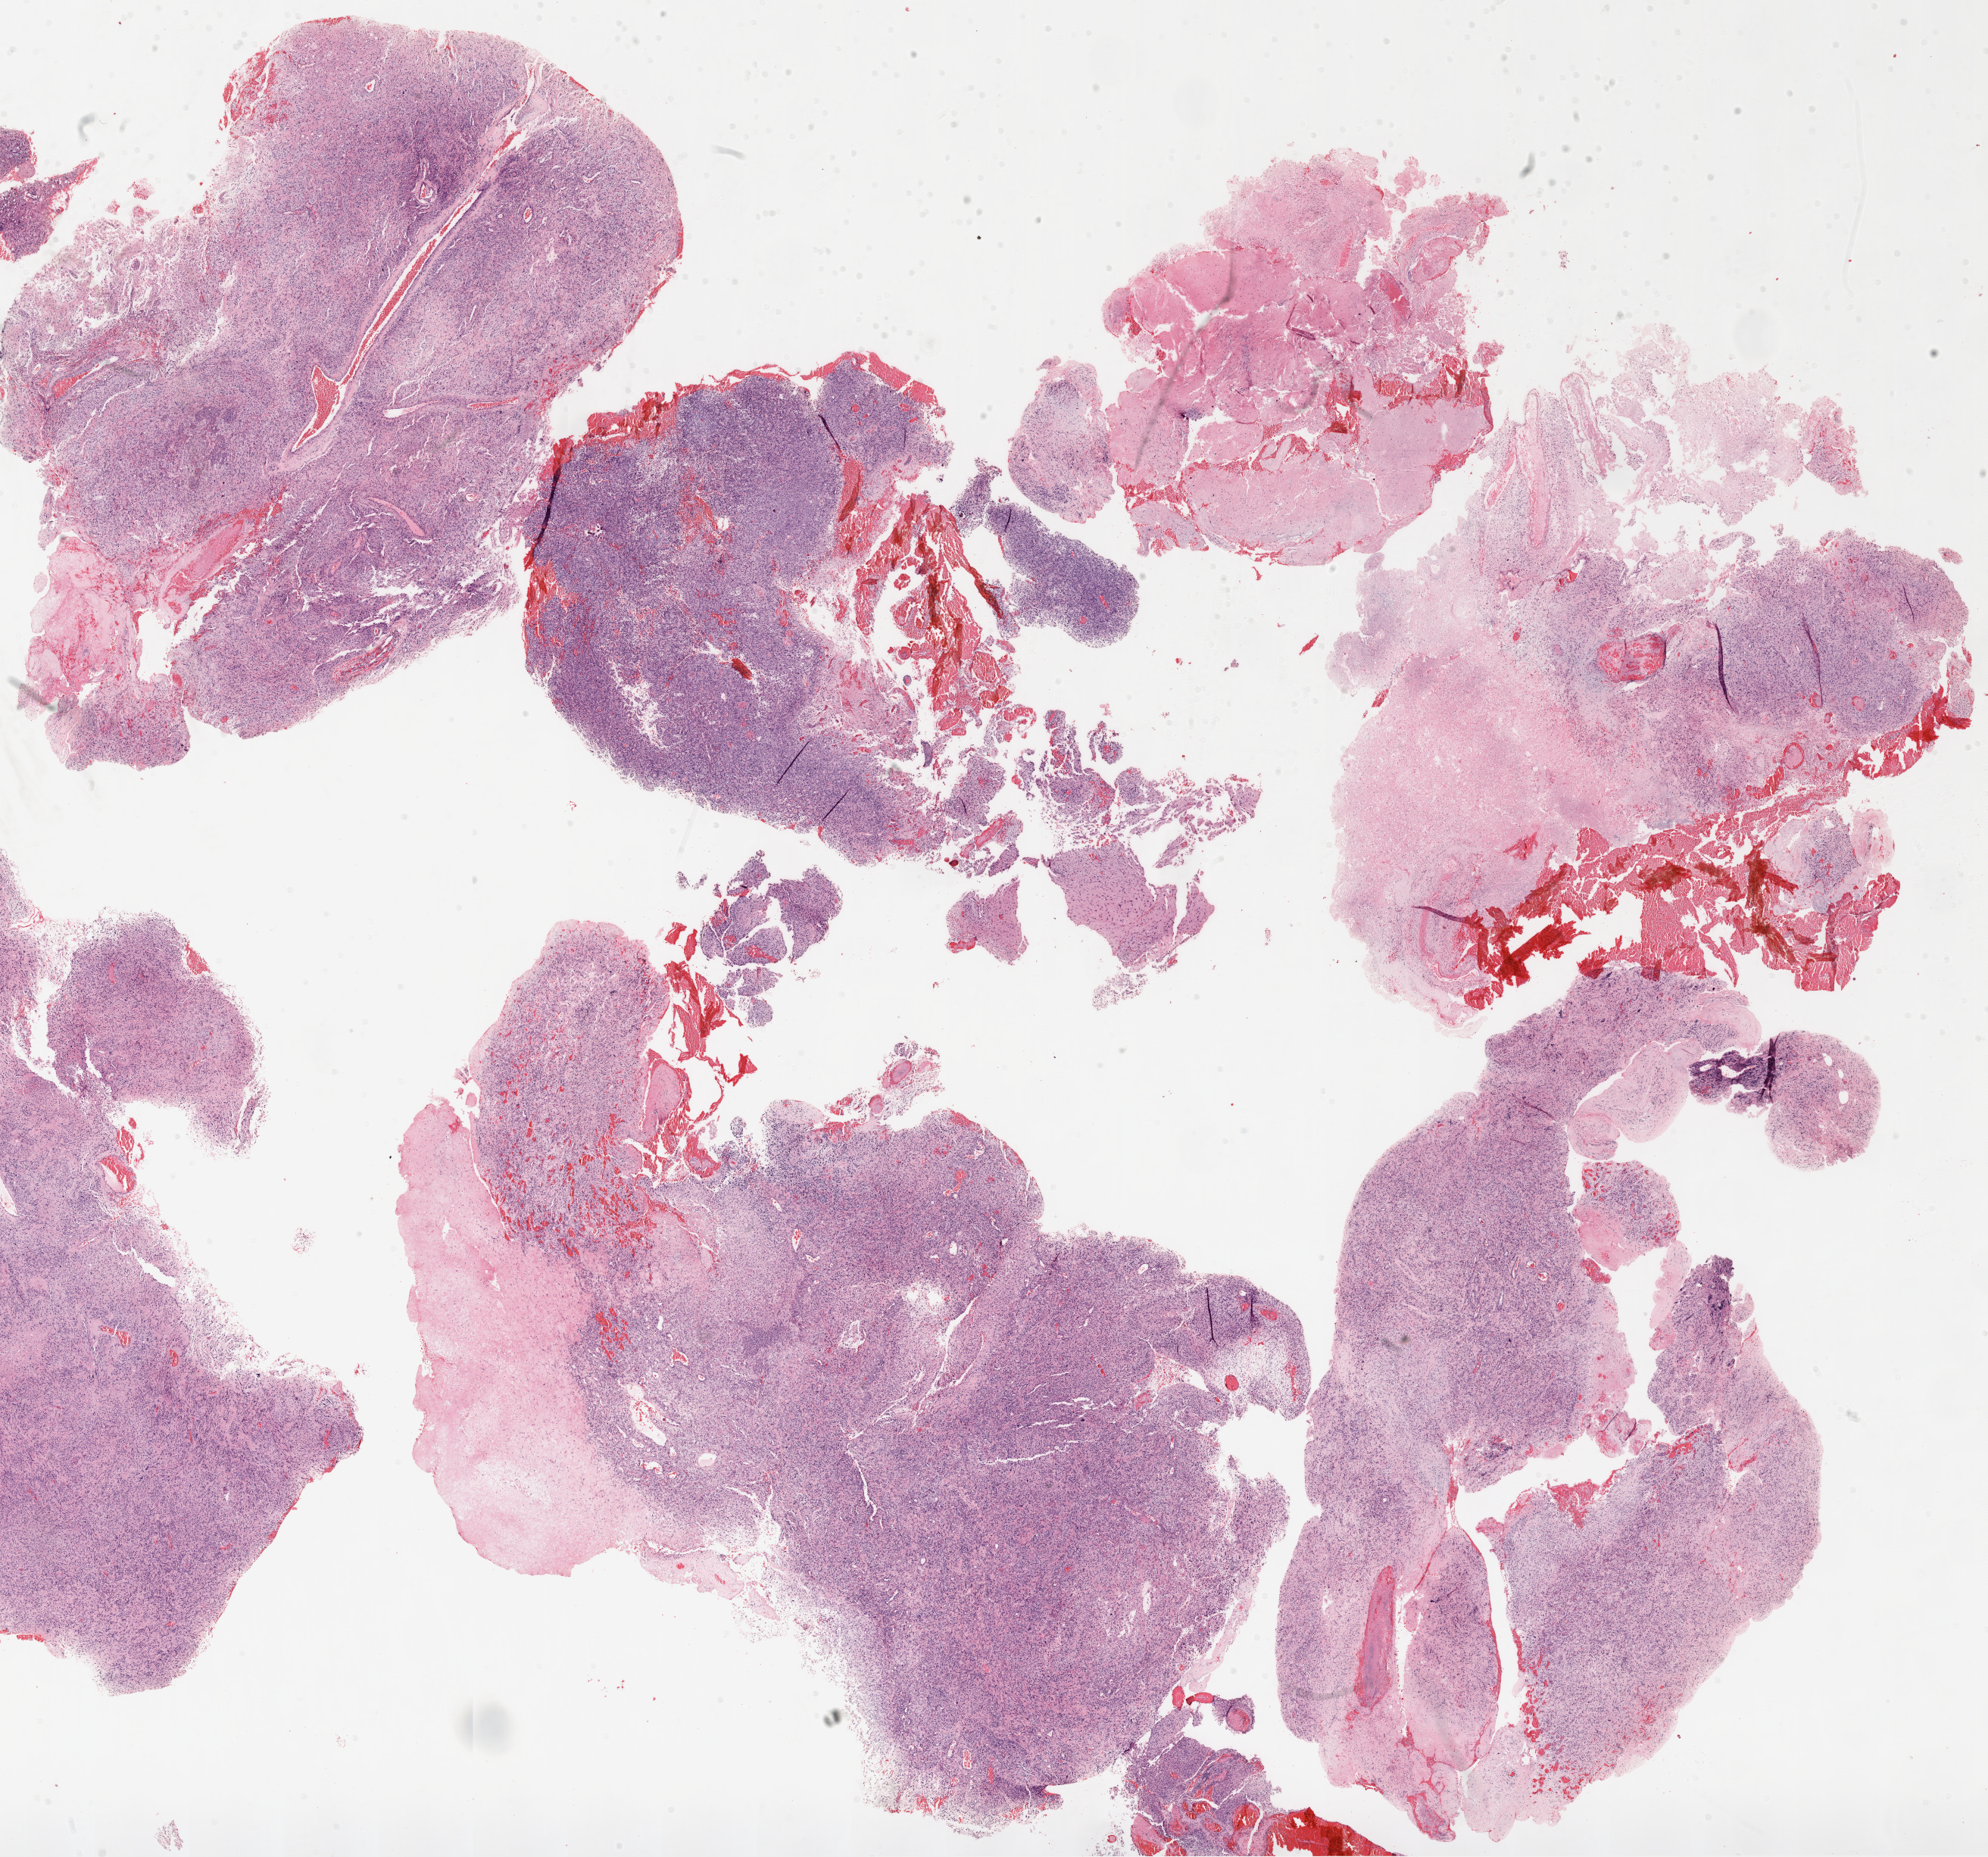
Digitized H&E-stained tissue section (whole slide) — whole scanned area (about 21.1 x 19.7 mm) shown as a low-resolution overview. Formalin-fixed paraffin-embedded (FFPE) diagnostic section. Sample: primary tumour, brain. Female, age 60 years at initial diagnosis.
* pathologic diagnosis: Glioblastoma